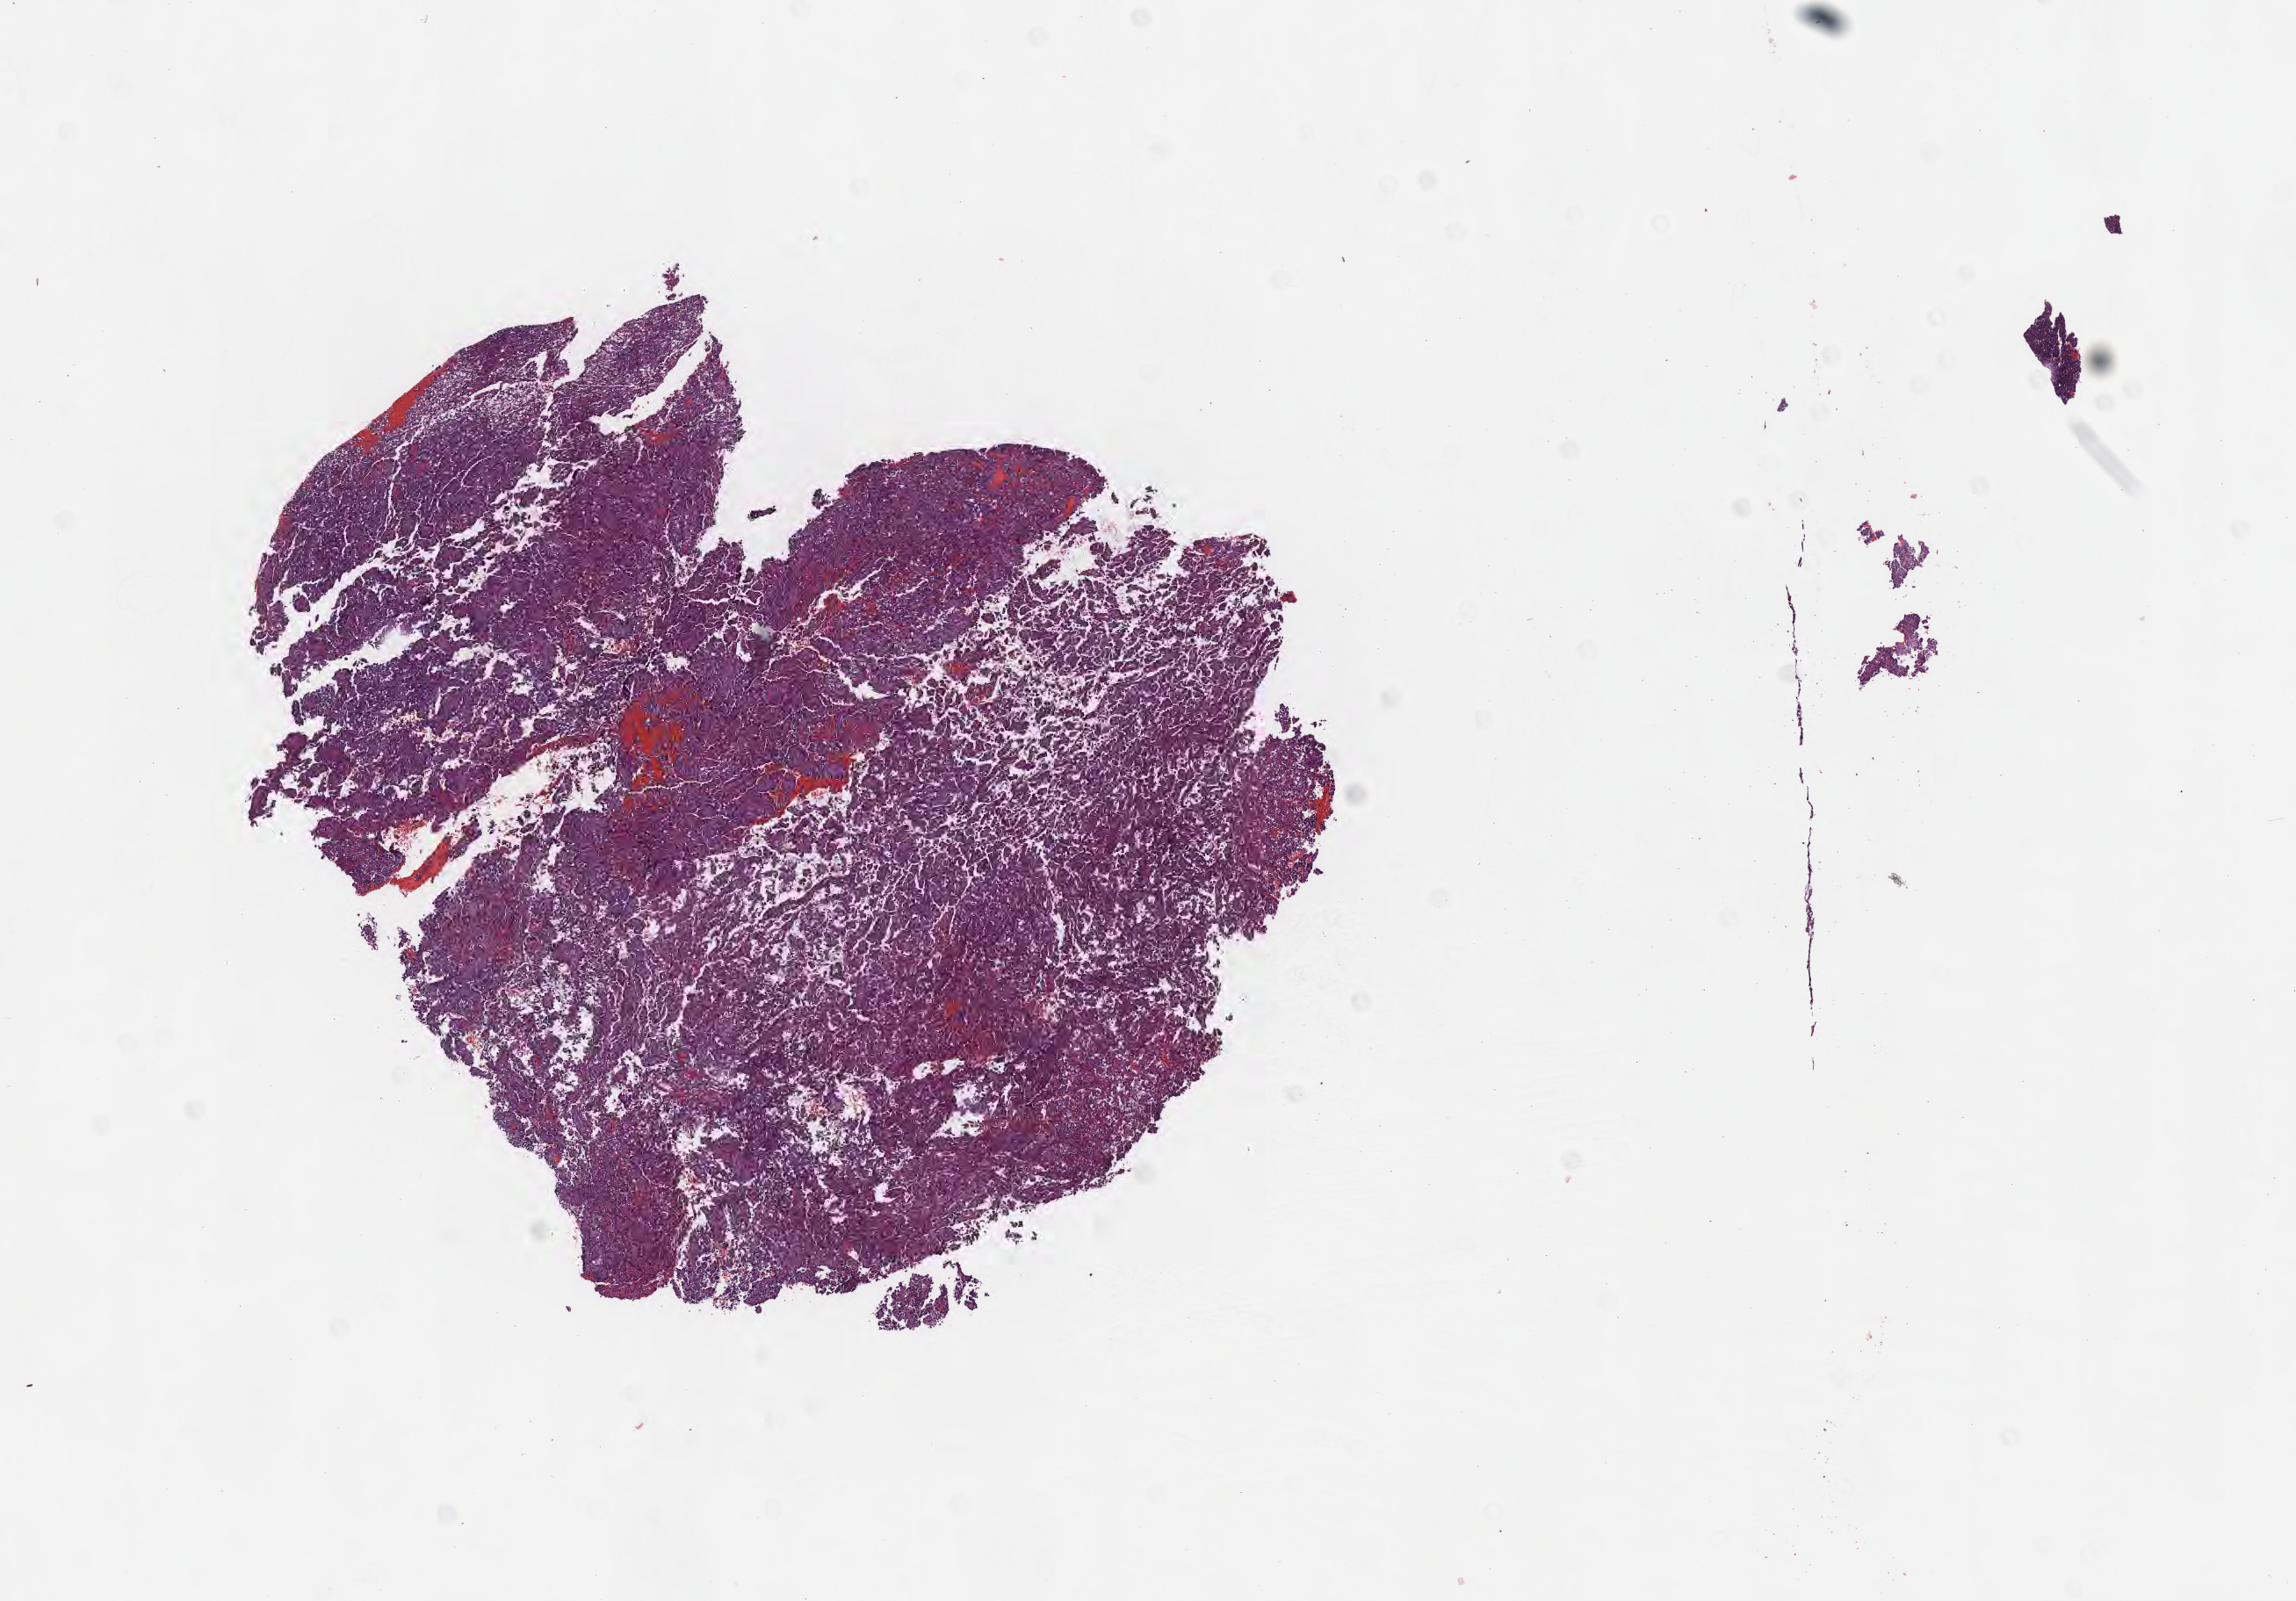
Whole-slide image, H&E stain of tumor tissue from the brain — a low-resolution overview of the entire scanned area, about 10.6 x 7.4 mm. FFPE section. Patient male; age 504 days (about 1.4 years).
Recorded diagnosis: Tumor cells, uncertain whether benign or malignant.